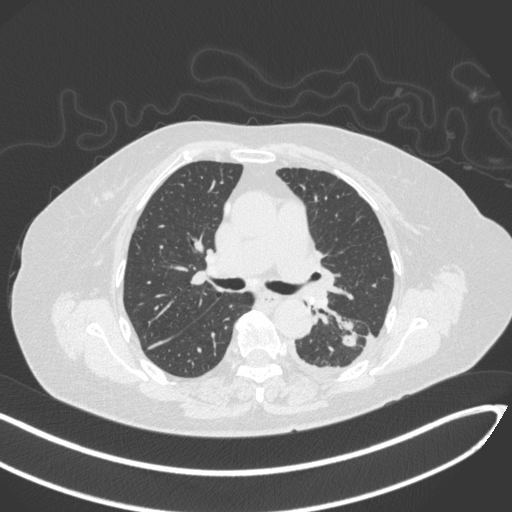
Chest CT, one axial slice; slice 192 of 270 in the series (ordered by position); reconstruction kernel B31f; lung window (W 1500 / L -600 HU); 1 mm slice thickness; 512 × 512 image matrix. Patient: female, 76 years. From the clinical record (not read from this slice): clinical TNM (as recorded): T1c N0 M0.
Annotated regions visible in this slice (bounding box drawn by a radiologist):
- lung tumour (recorded histology: adenocarcinoma): box from (x=338, y=329) to (x=361, y=350) px